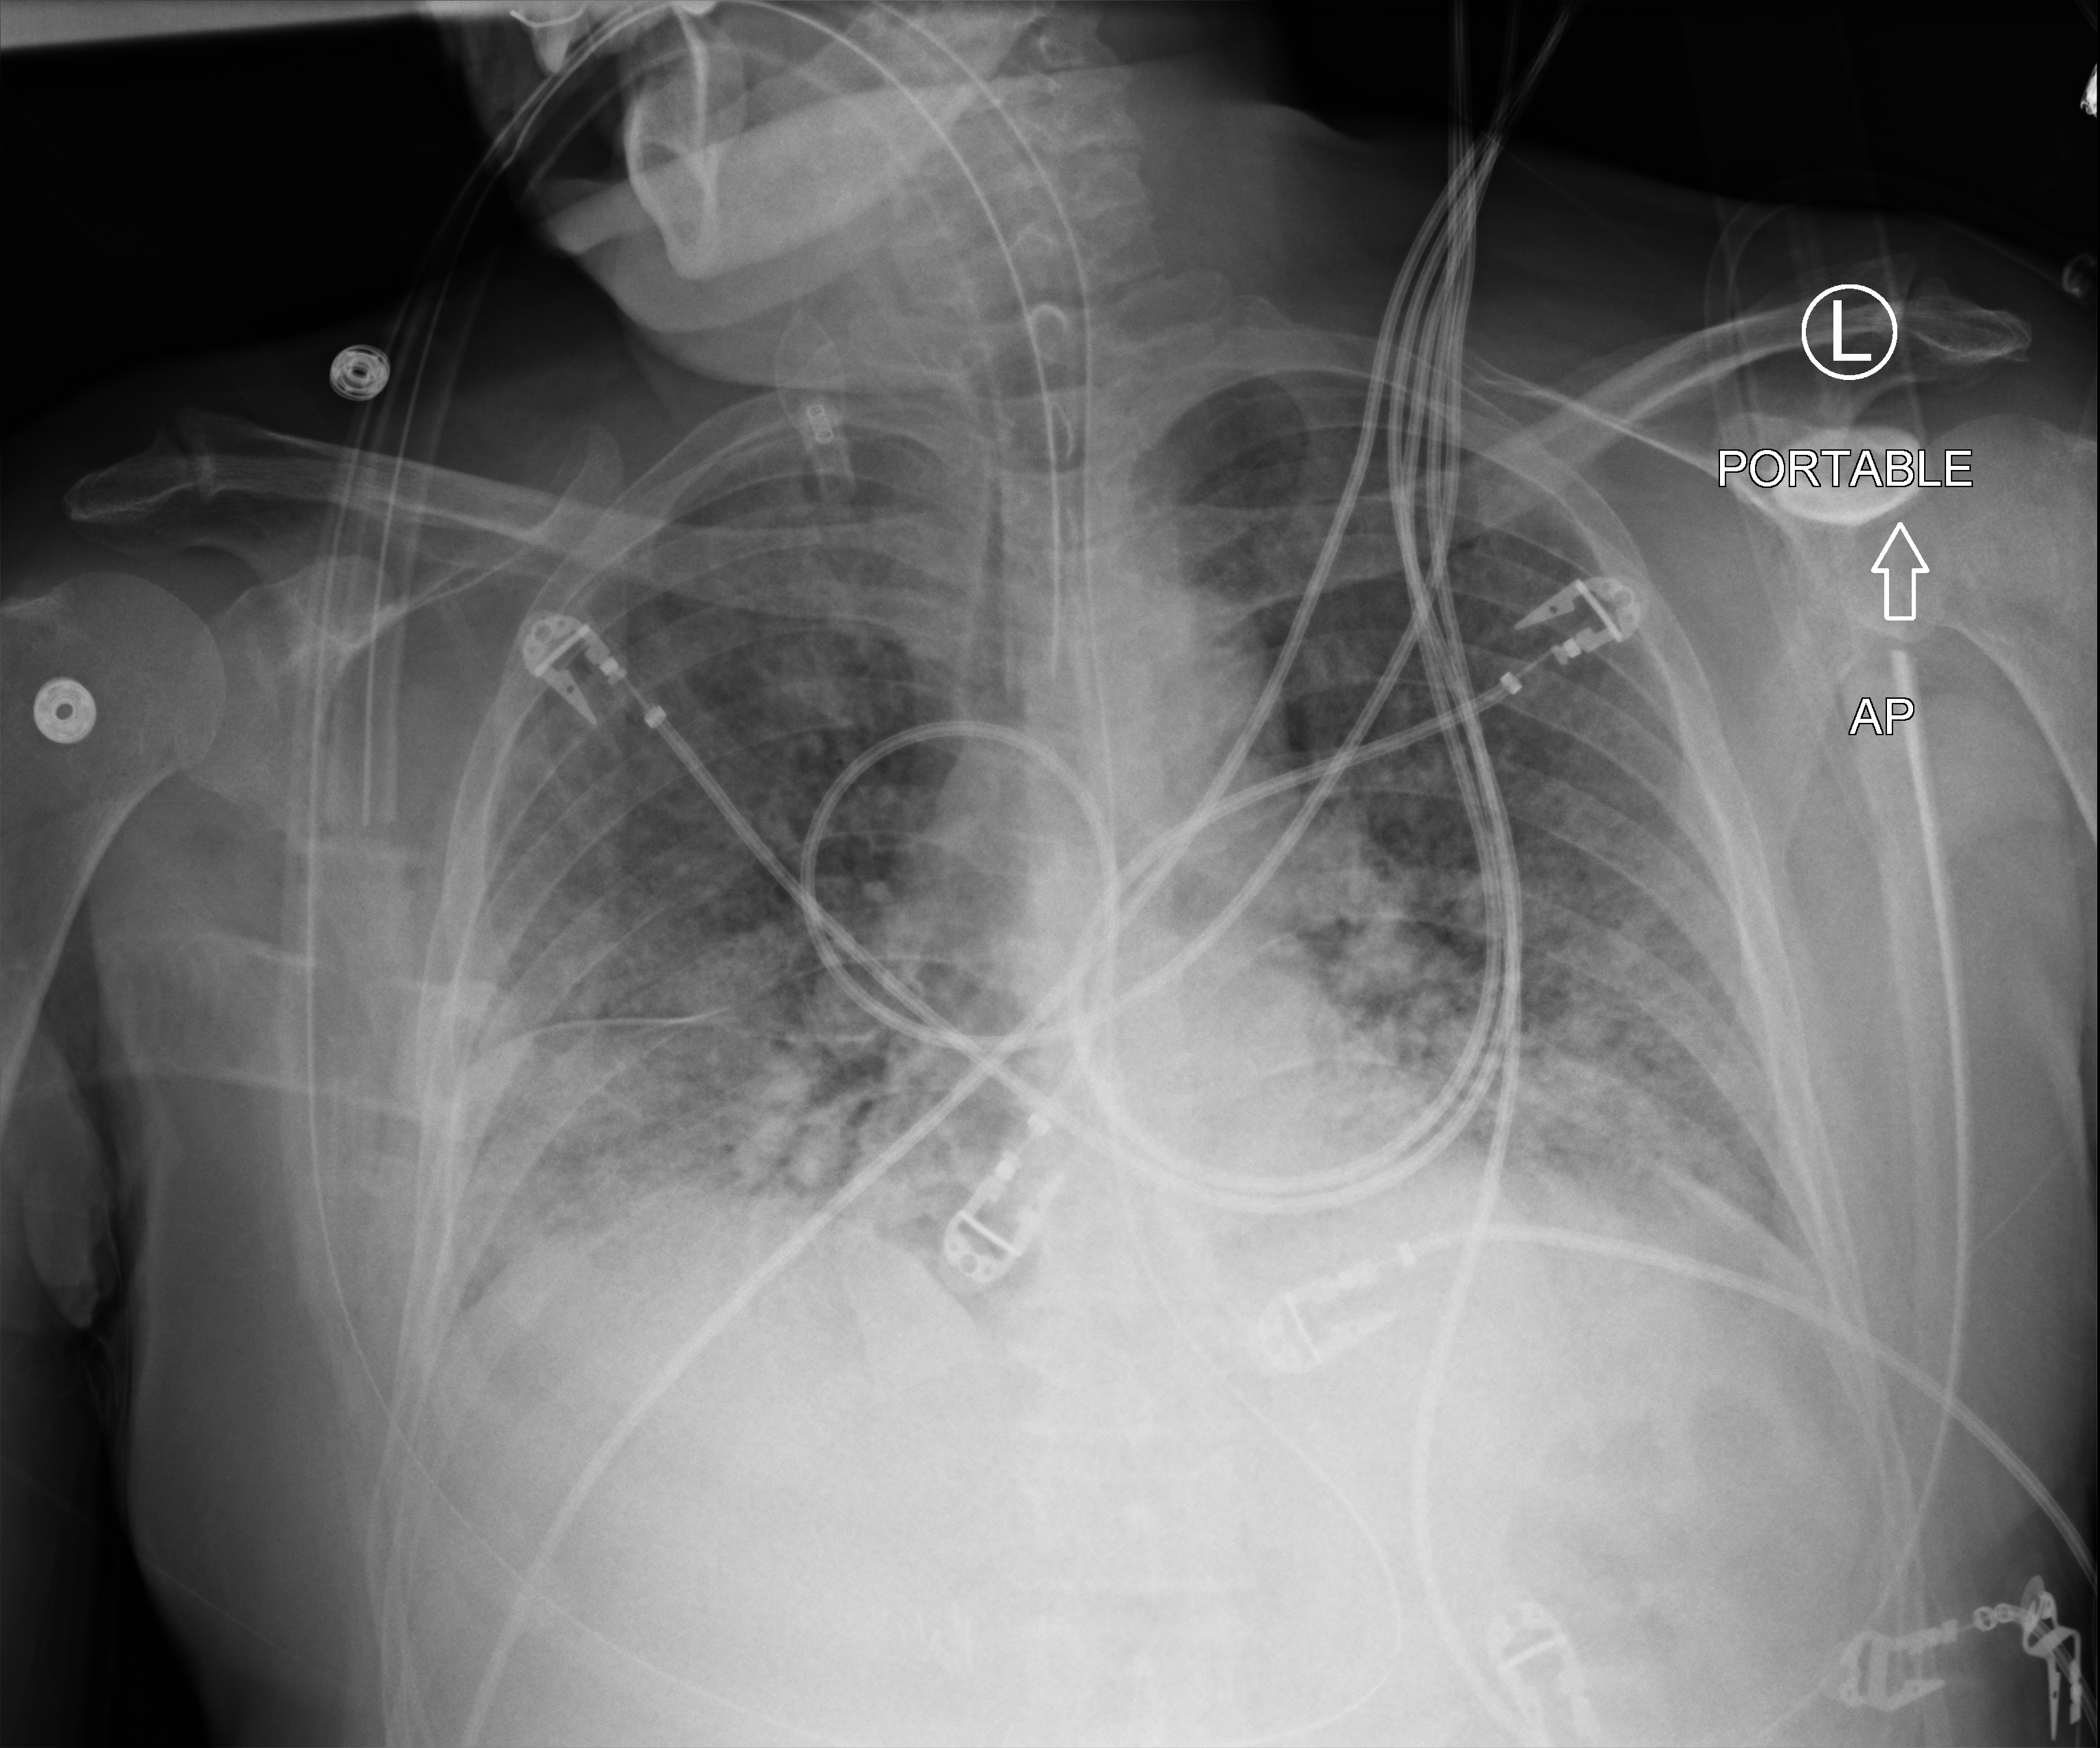
Bedside chest radiograph (computed radiography). Patient hospitalised with COVID-19; male, aged 60–74 years.
Hospital-stay facts (about this admission, not read from this image; timing relative to this image not recorded): mechanically ventilated during this hospital stay: yes; hypertension (admission record): no.